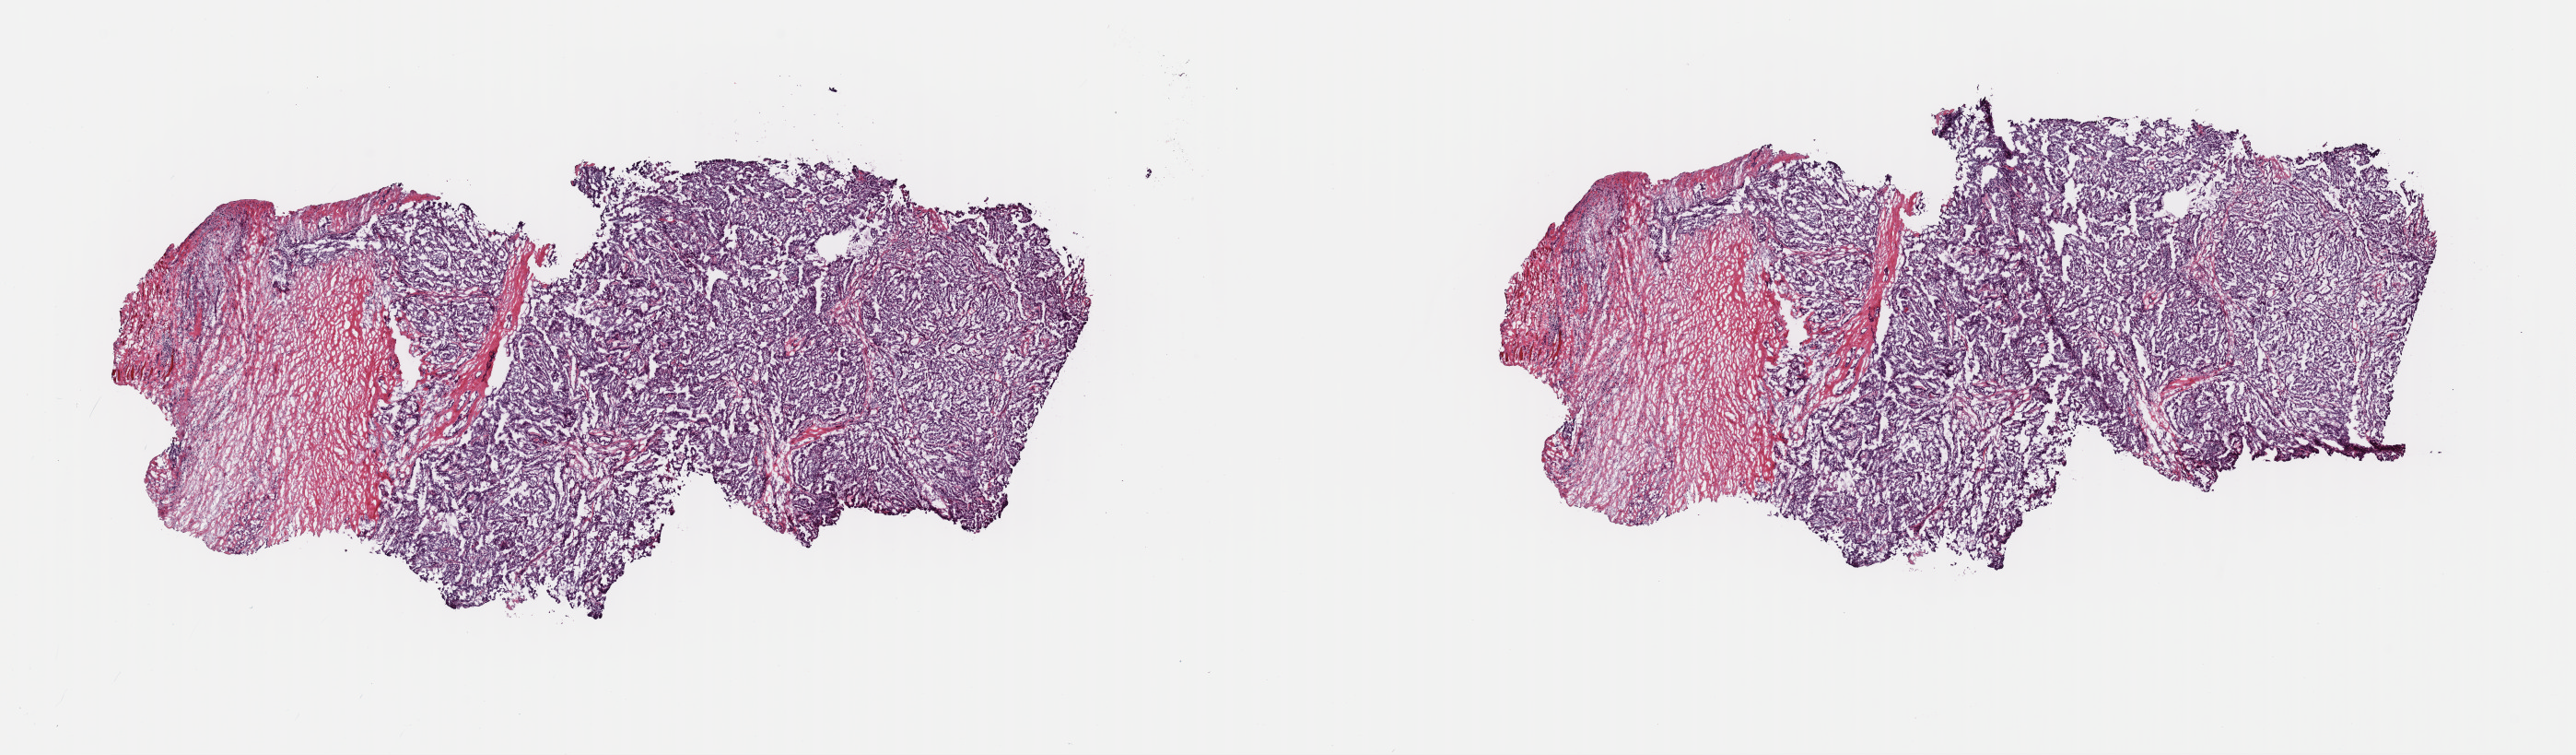
H&E-stained whole-slide image, a low-resolution overview of the entire scanned area, about 22.1 x 6.5 mm (from a 40x scan); frozen section; thyroid, primary tumour sample. Female patient; age at initial diagnosis 47 years. Slide review estimates, as recorded: tumour cells 75%, tumour nuclei 88%, normal cells 0%, stromal cells 25%, necrosis 0%. Infiltration values recorded for this section: lymphocyte infiltration 0%, monocyte infiltration 0%, neutrophil infiltration 0%.
* AJCC pathologic stage: II (5th edition)
* histologic diagnosis: Papillary adenocarcinoma, NOS